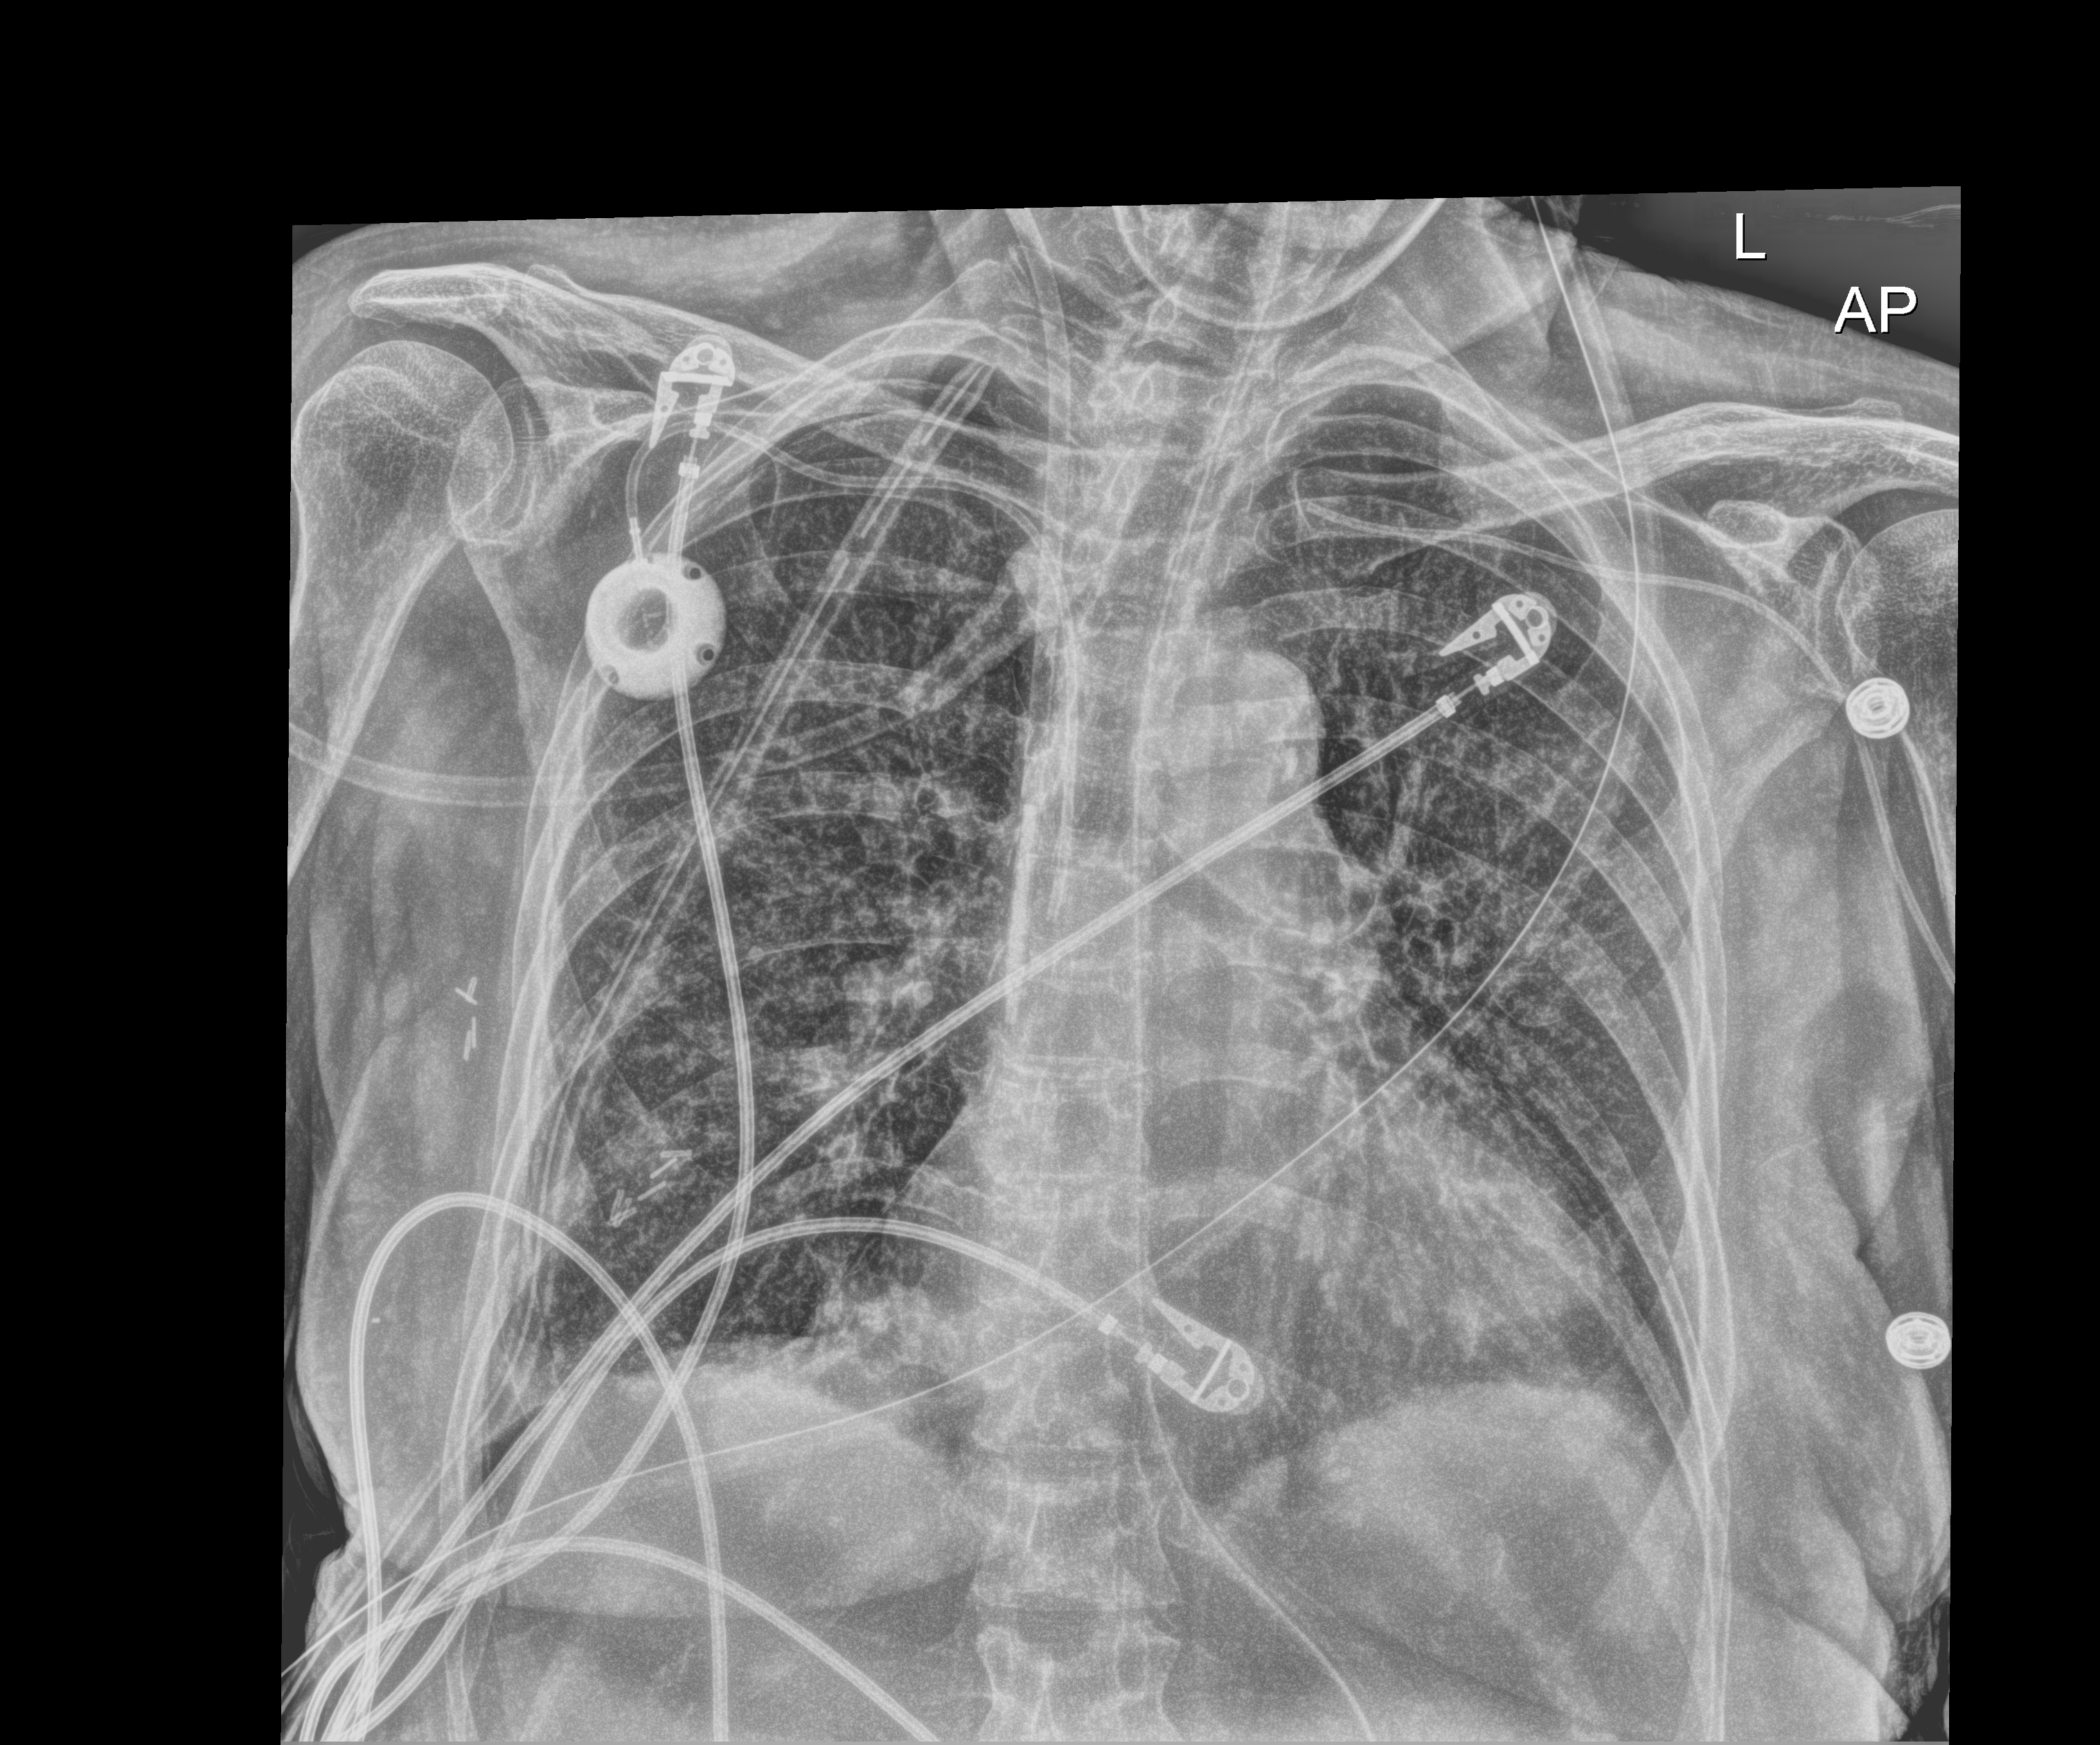
Chest X-ray (portable), anteroposterior (AP) projection. Patient hospitalised with COVID-19; female, aged 60–74 years.
Hospital-stay facts (about this admission, not read from this image; timing relative to this image not recorded): diabetes (admission record): no.